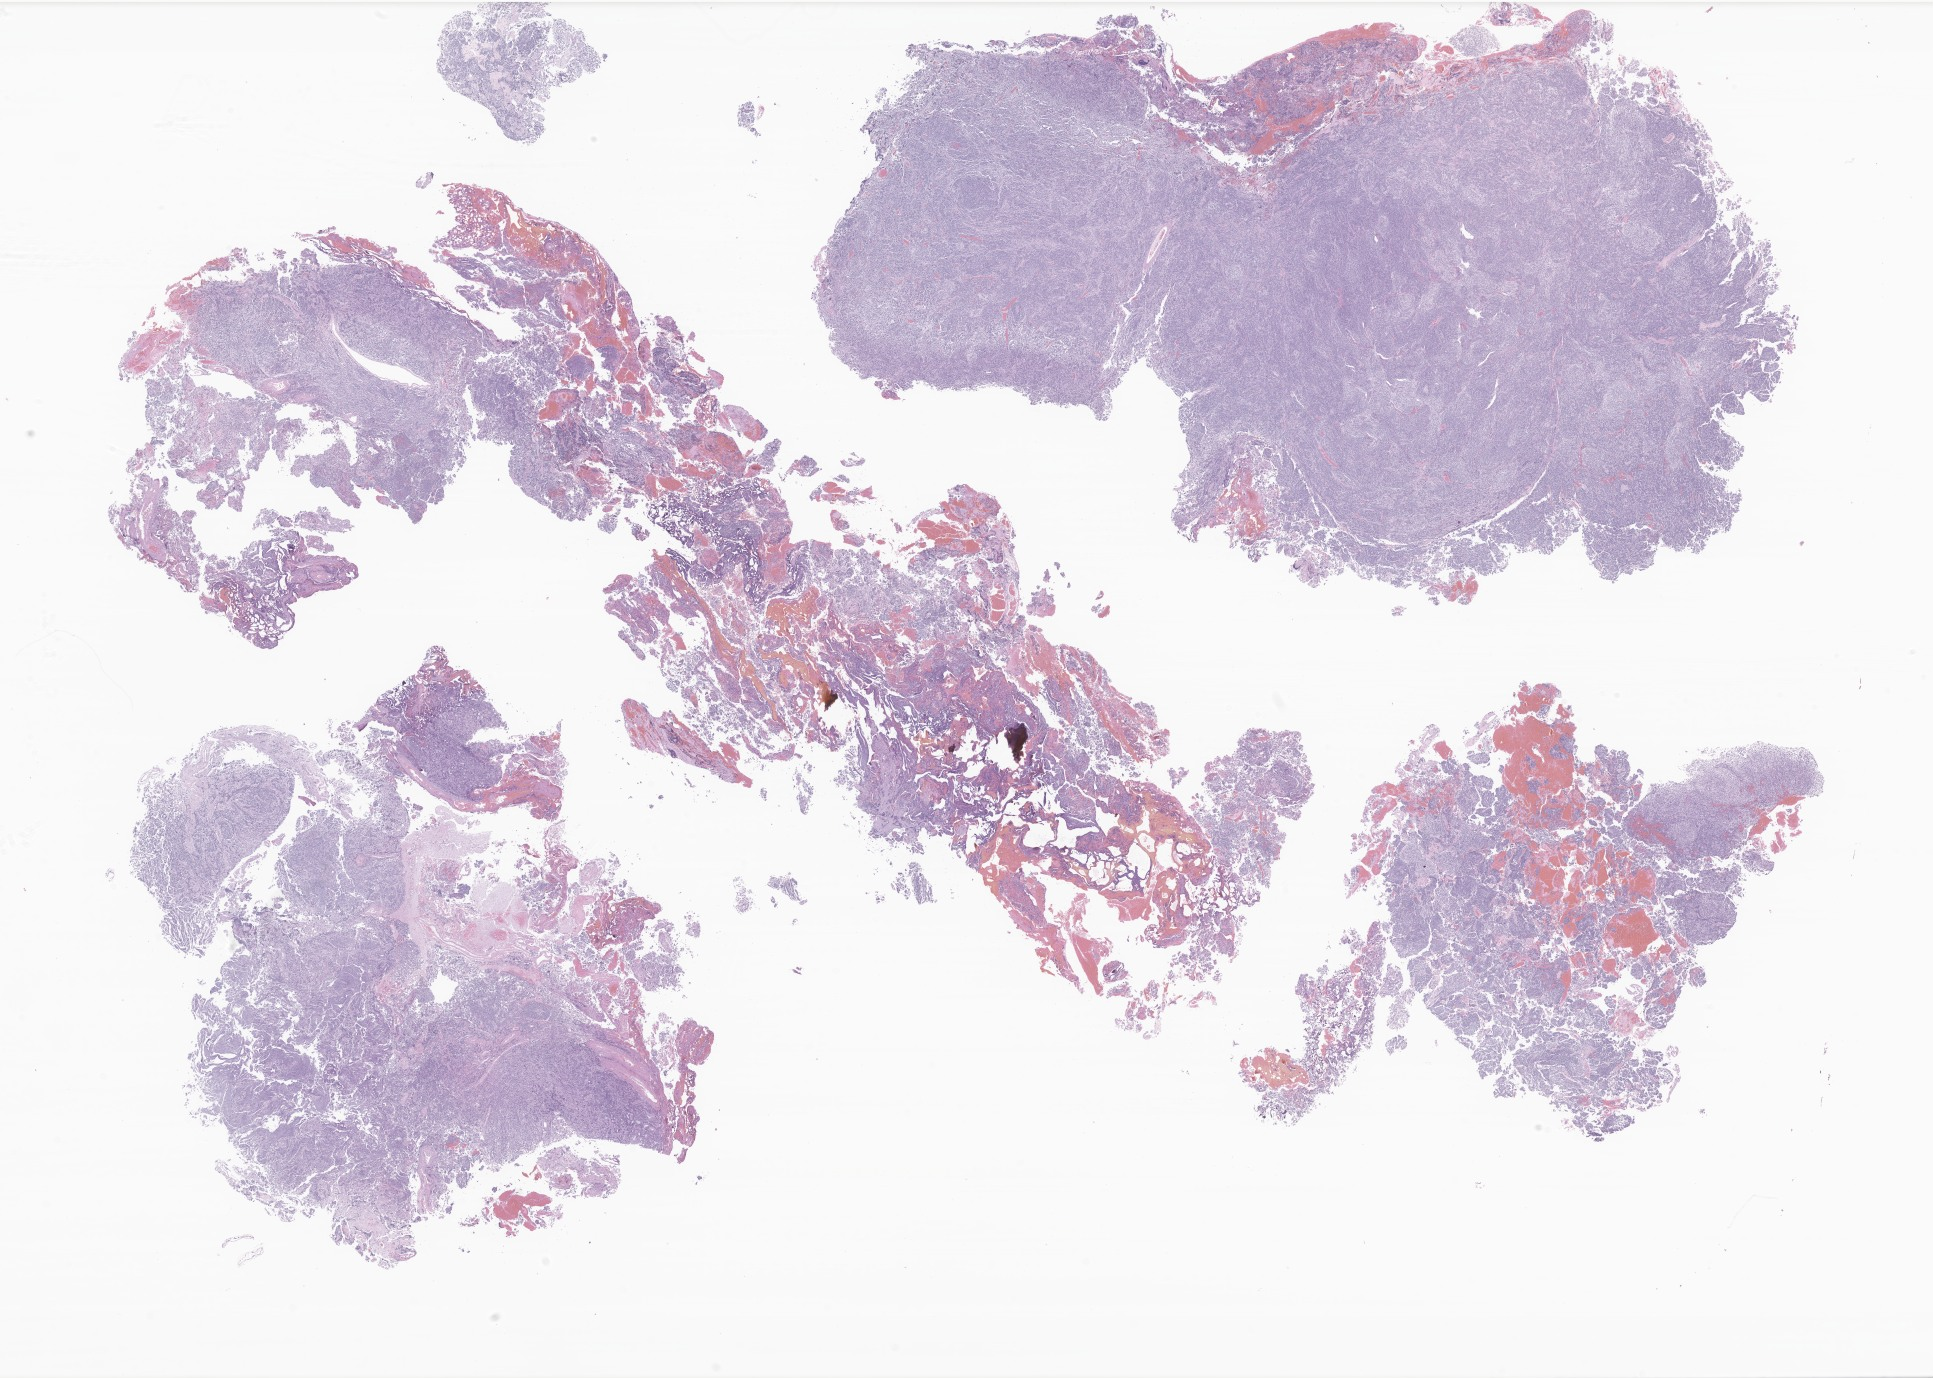
Haematoxylin and eosin whole-slide image of tumor tissue from the brain — whole scanned area (about 32.6 x 23.2 mm) shown as a low-resolution overview; formalin-fixed paraffin-embedded section. Male patient, age 90 months (7 years 6 months).
Recorded diagnosis: Medulloblastoma, NOS.